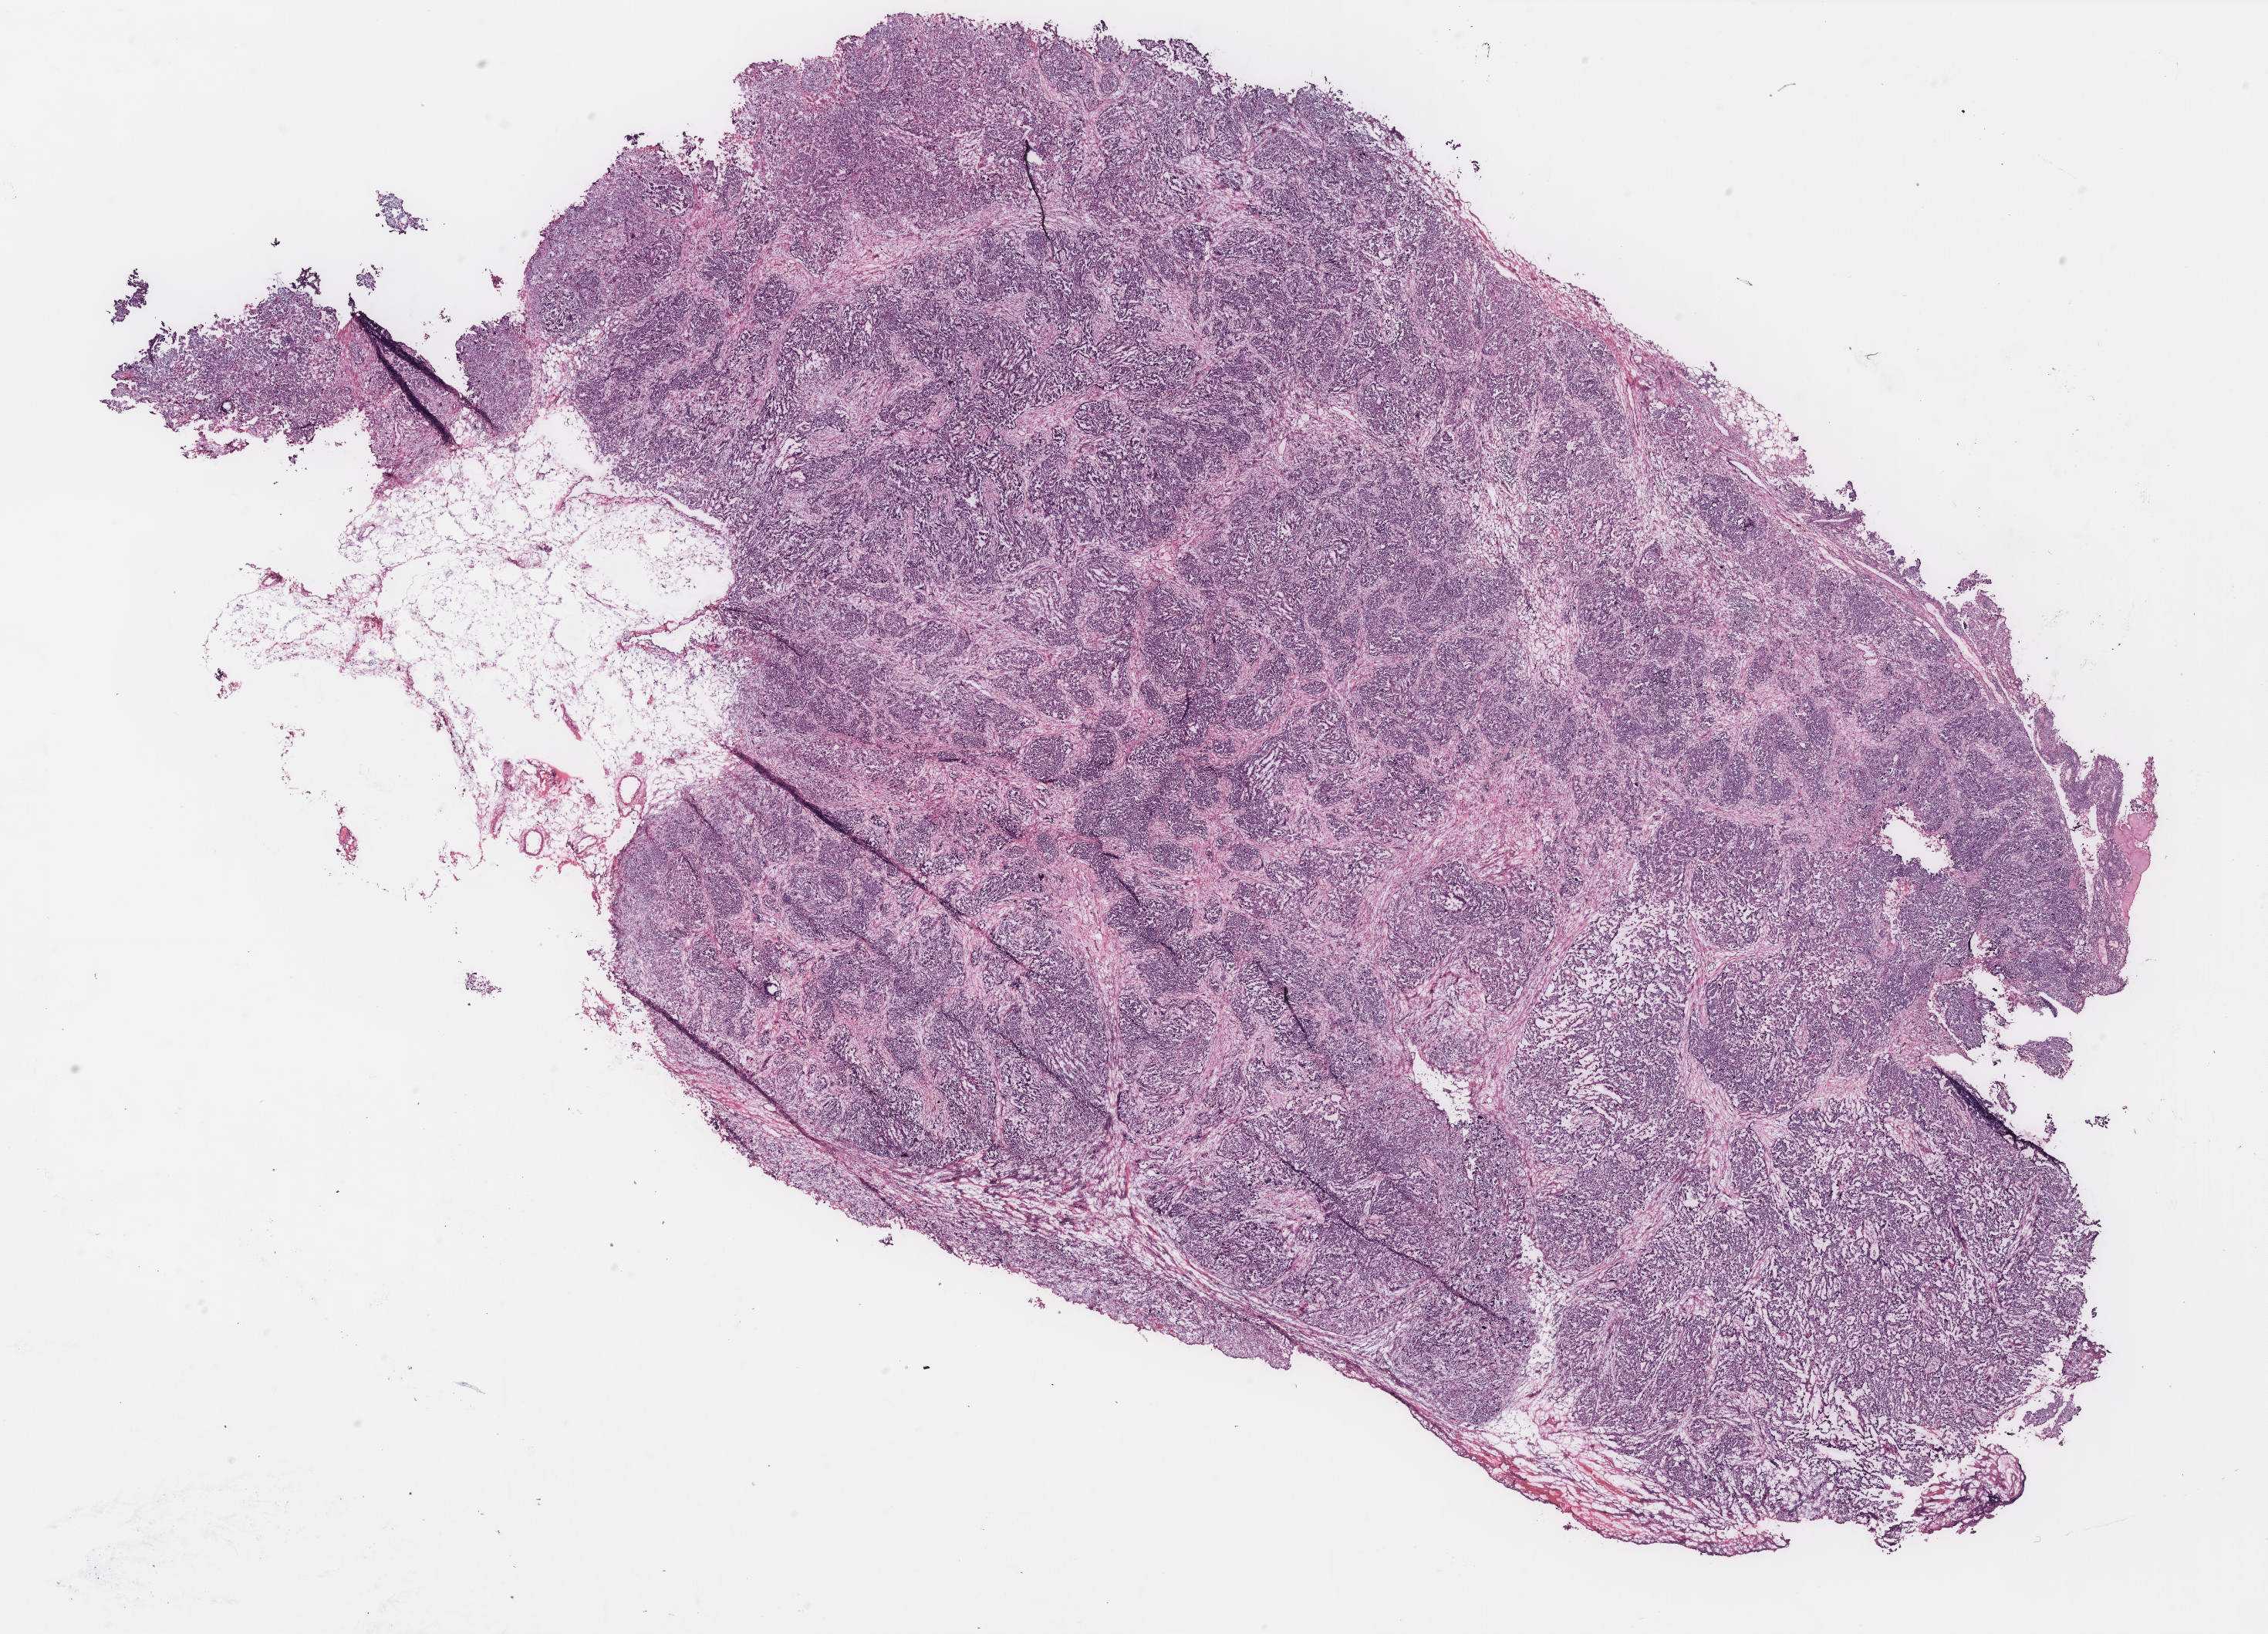
Whole-slide histology image, Hematoxylin and eosin (H&E) stained, low-resolution overview of the scanned area, about 23.5 x 17.0 mm. Normal (non-tumour) tissue sample, ovary. Female, 65 y/o.
This section: normal (non-tumour) tissue from the same patient. Patient diagnosis: Serous adenocarcinoma, NOS.